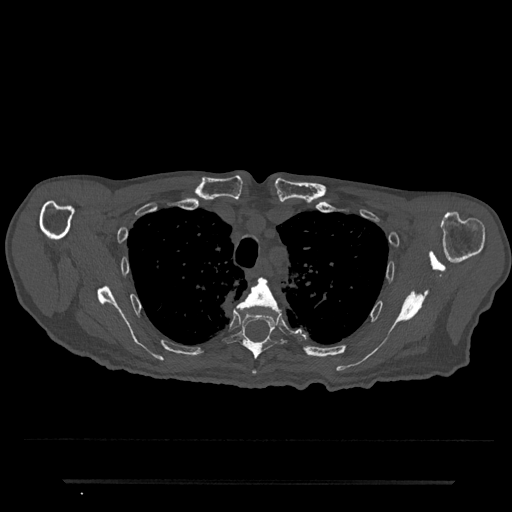
CT including the spine, one axial slice. 120 kVp. Bone window (W 1800 / L 400 HU). 0.5 mm slice thickness. 512 × 512 image matrix, field of view 427 × 427 mm. Patient: male, 74 years. From the clinical record (not read from this slice): primary cancer: prostate.
Structures marked on this image (semi-automatically segmented with operator editing):
- T4 vertebra: bounding box <239,278,282,374> (left, top, right, bottom; pixels)
- T5 vertebra: <222,303,283,360>